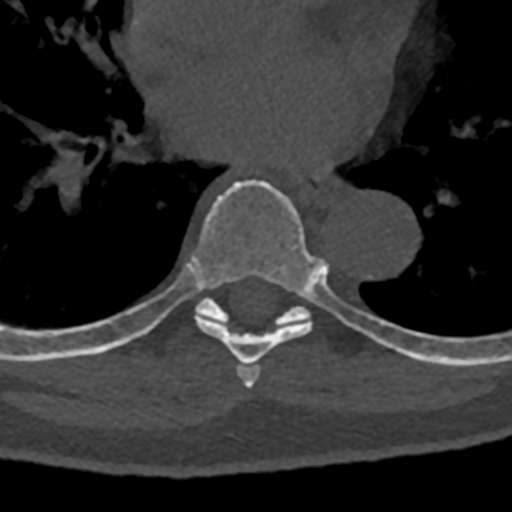
CT including the spine, one axial slice. Slice 747 of 797 in the series (ordered by position). Reconstruction kernel Br40s/3. Bone window (W 1800 / L 400 HU). 0.5 mm slice thickness. 512 × 512 image matrix, field of view 160 × 160 mm. Male patient, age 74 years. From the clinical record (not read from this slice): primary cancer: renal; vertebrae with lytic lesions (as recorded): T10, L1, L2, L3, L4, L5.
Structures marked on this image (semi-automatically segmented with operator editing):
- T6 vertebra: bounding box [x1, y1, x2, y2] px = [237, 365, 260, 389]
- T7 vertebra: [71, 180, 389, 366]
- T8 vertebra: [70, 297, 432, 363]